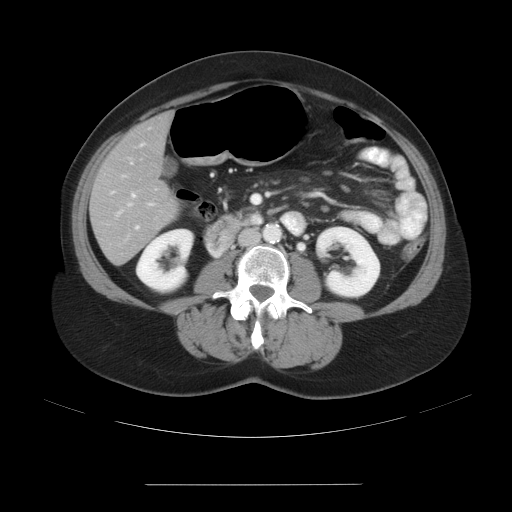
Contrast-enhanced abdominal CT, one axial slice. Slice 8 of 27 in the series (ordered by position). Intravenous contrast given. Soft-tissue window (W 400 / L 40 HU). 7.5 mm slice thickness. 512 × 512 image matrix, field of view 440 × 440 mm. Female patient, age 58 years. Case-level facts recorded for this patient, not image findings: diagnosis: colorectal cancer liver metastases, imaged before liver resection; multiple liver metastases: yes; largest metastasis: 1.9 cm; disease in both lobes: yes.
Outlined on this slice (expert manual segmentation):
- hepatic veins: bounding box <129,194,135,206> (left, top, right, bottom; pixels)
- liver: <92,114,176,264>
- planned liver remnant (the part of the liver to remain after resection): <96,114,171,194>
- portal vein (with intrahepatic branches): <112,142,153,229>